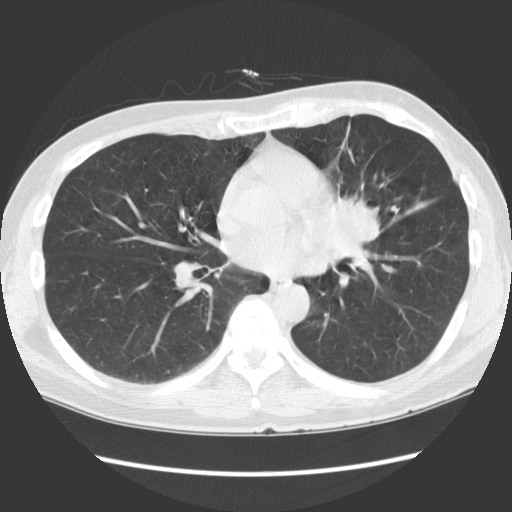
Low-dose screening chest CT, one axial slice. Position 65 of 136 along the scan axis. Reconstruction kernel STANDARD. 140 kVp. Lung window (W 1500 / L -600 HU). 2.5 mm slice thickness. 512 × 512 image matrix, field of view 360 × 360 mm.
Annotated regions visible in this slice (expert manual segmentation):
- lesion 1 (tumor, hilum of left lung): bounding box [x1, y1, x2, y2] px = [332, 197, 380, 241]